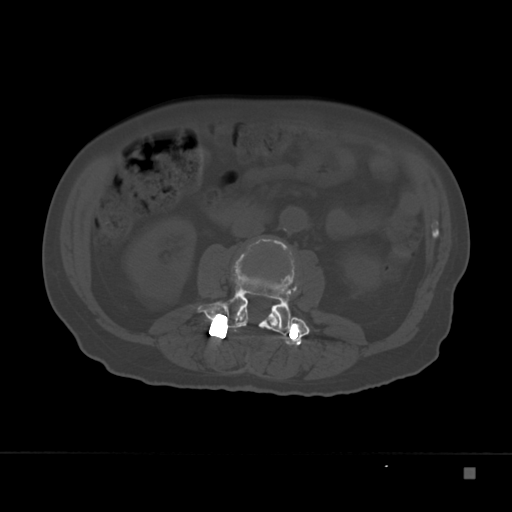
CT including the spine, one axial slice. Slice 76 of 332 in the series (ordered by position). Bone window (W 1800 / L 400 HU). 512 × 512 image matrix. Male patient, age 72 years. Case-level facts recorded for this patient, not image findings: primary cancer: skeletal.
Annotated regions visible in this slice (semi-automatic segmentation, software-assisted and operator-edited):
- L2 vertebra: bounding box (x1, y1, x2, y2) in pixels: (236, 240, 286, 328)
- L3 vertebra: (197, 258, 310, 336)